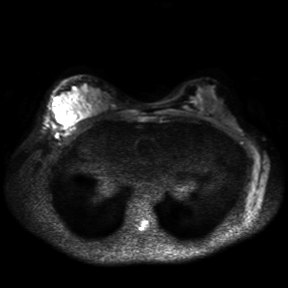
Breast MRI, one axial slice; position 20 of 30 along the scan axis; diffusion-weighted series; image 2 of 4 stored at this slice position (different b-values; order by instance number); 3 T; 4 mm slice thickness; 288 × 288 image matrix. Female patient.
Outlined on this slice (manually delineated by an expert):
- tumour on diffusion-weighted imaging: bounding box [x1, y1, x2, y2] px = [53, 108, 64, 124]